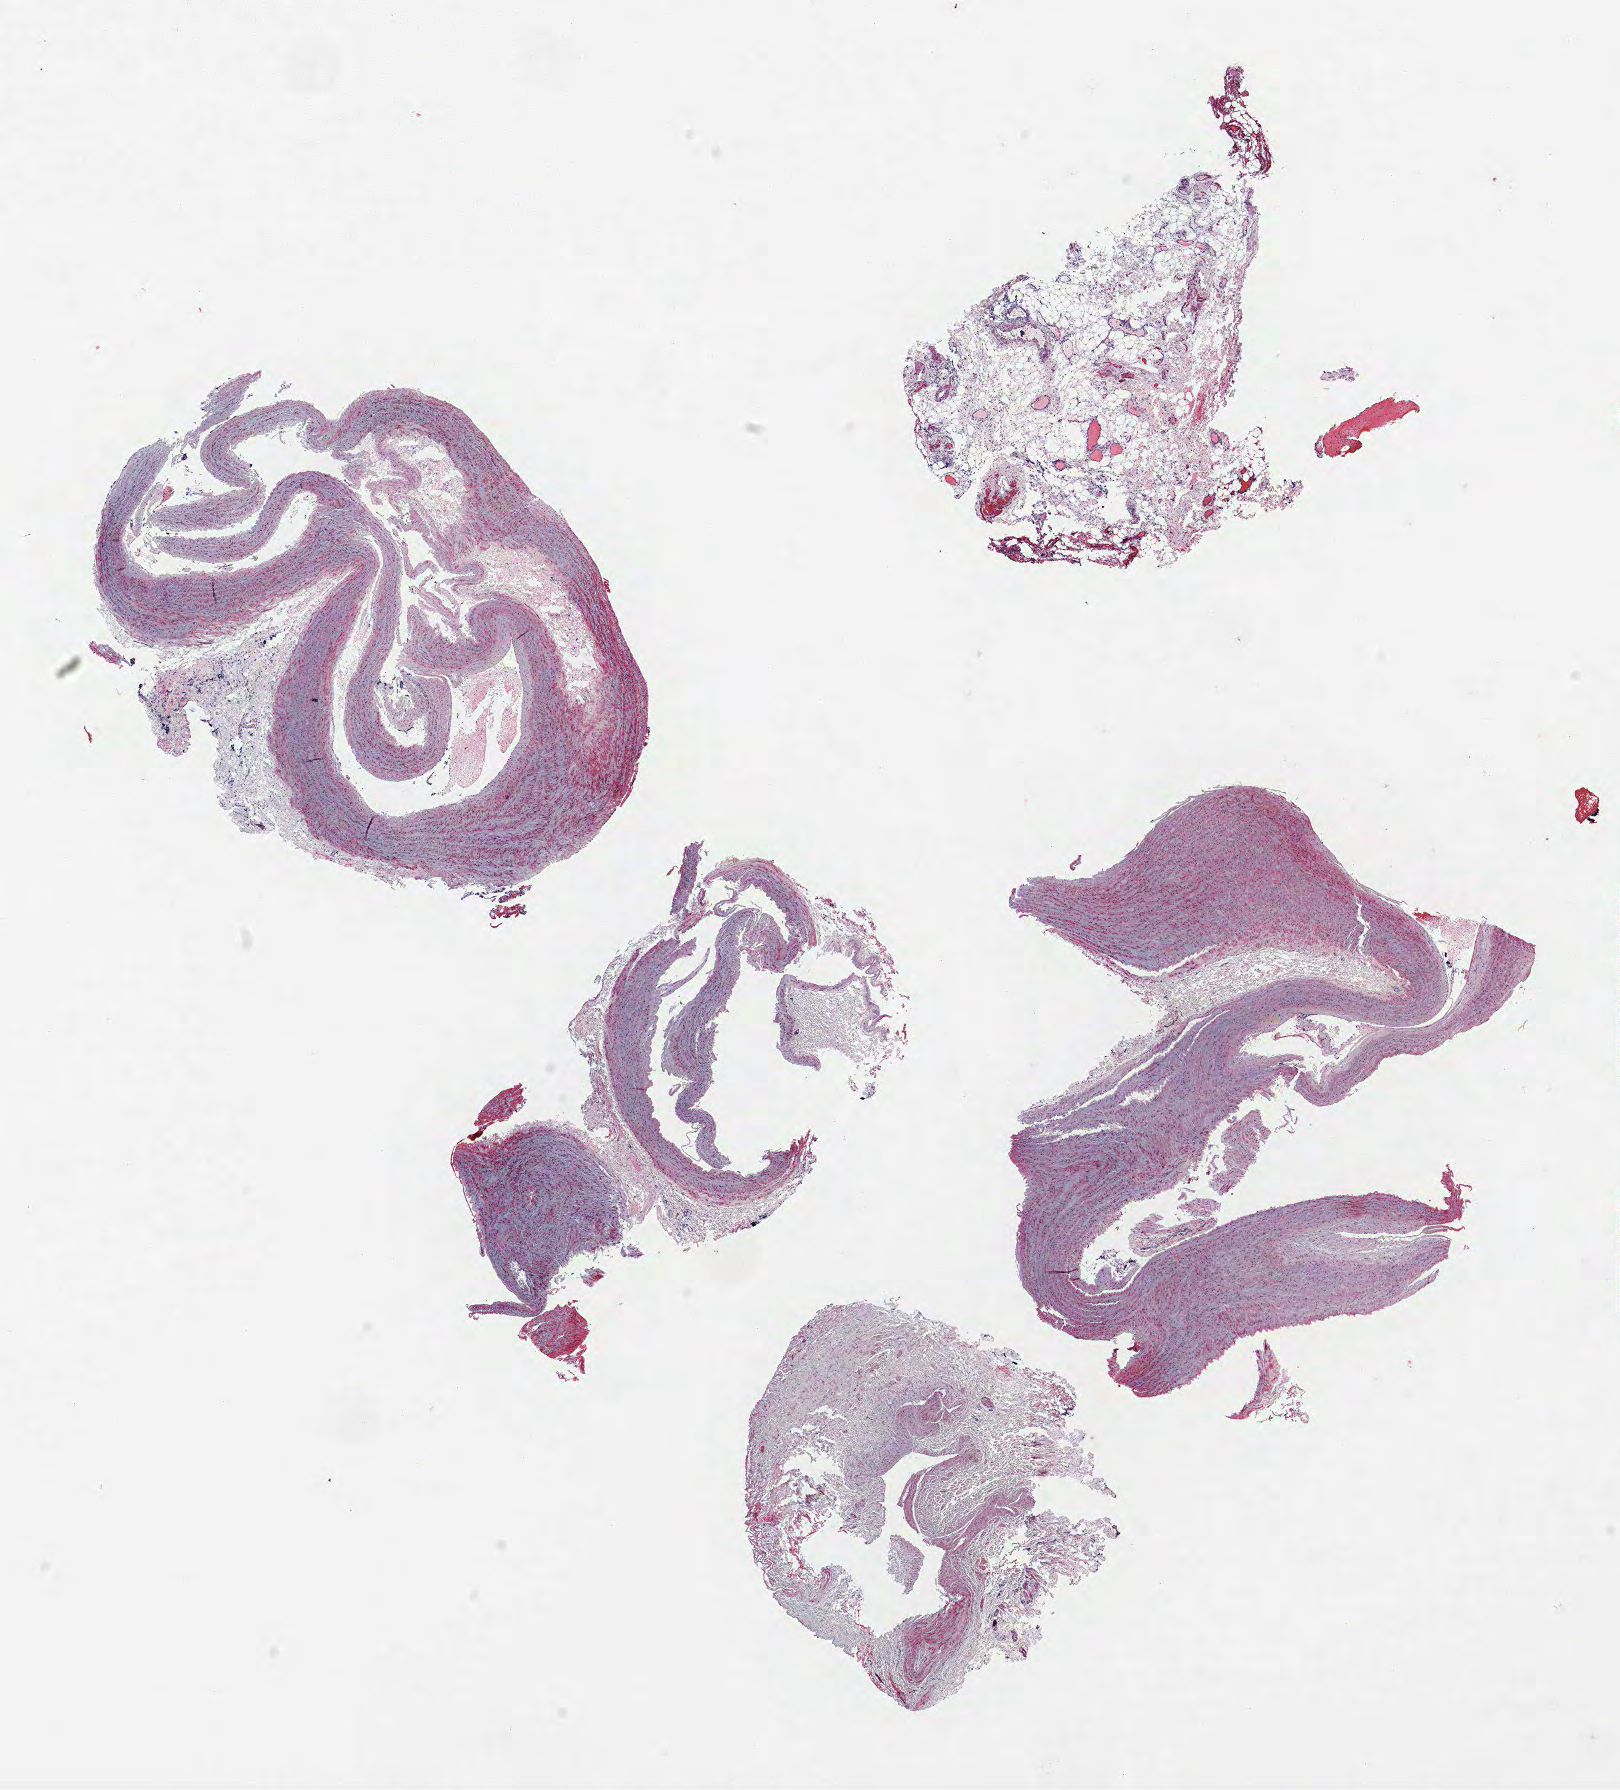
H&E whole-slide image, whole scanned area (about 13.0 x 14.3 mm, slide scanned at 40x) shown as a low-resolution overview; formalin-fixed paraffin-embedded (FFPE) section; lung tissue. Female patient, aged 67 at enrolment. Current smoker at enrolment.
Participant's lung-cancer diagnosis: Adenocarcinoma, NOS (ICD-O-3 8140/3). Note: participant had 2 primary lung cancers recorded; fields above describe the first.